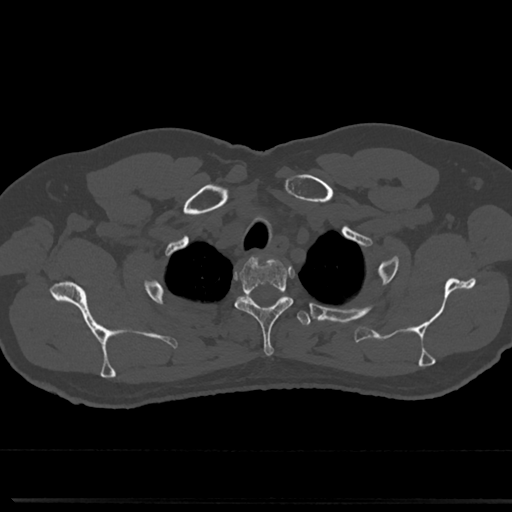
CT including the spine, one axial slice; position 628 of 817 along the scan axis; reconstruction kernel Br40s/3; 120 kVp; bone window (W 1800 / L 400 HU); 0.5 mm slice thickness; 512 × 512 image matrix, field of view 355 × 355 mm. Male patient, age 61 years. Case-level facts recorded for this patient, not image findings: primary cancer: prostate.
Outlined on this slice (semi-automatically segmented with operator editing):
- T1 vertebra: bounding box <239,296,287,305> (left, top, right, bottom; pixels)
- T2 vertebra: <235,254,292,357>
- T3 vertebra: <243,297,311,328>